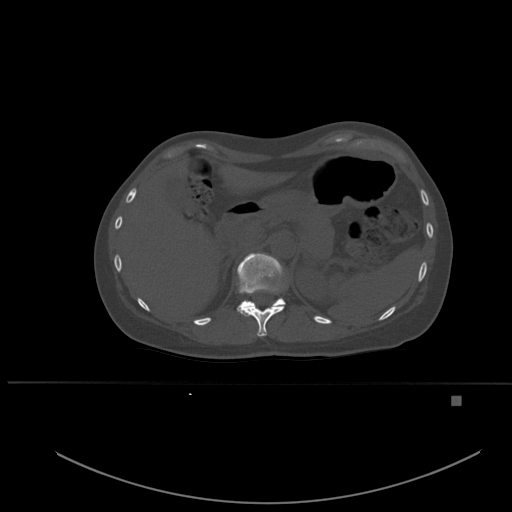
CT including the spine, one axial slice; position 264 of 651 along the scan axis; bone window (W 1800 / L 400 HU); 1.5 mm slice thickness; 512 × 512 image matrix, field of view 443 × 443 mm. Female patient, age 49 years. From the clinical record (not read from this slice): primary cancer: breast; vertebrae with lytic lesions (as recorded): L3, T12, L4.
Annotated regions visible in this slice (semi-automatically segmented with operator editing):
- T11 vertebra: box from (x=237, y=282) to (x=284, y=337) px
- T12 vertebra: (x=237, y=253)–(x=286, y=312)